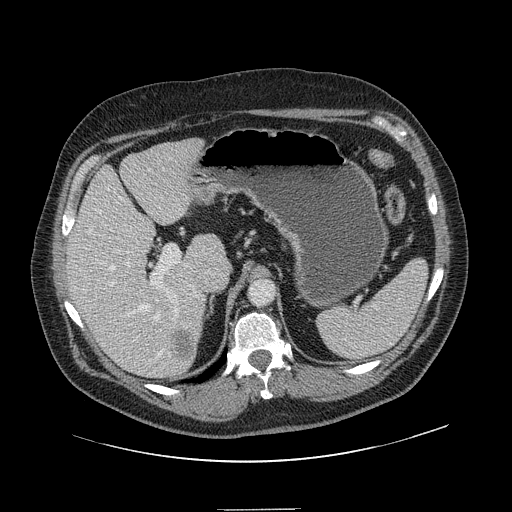
Contrast-enhanced abdominal CT, one axial slice. Slice 93 of 154 in the series (ordered by position). Intravenous contrast given. Soft-tissue window (W 400 / L 40 HU). 512 × 512 image matrix, field of view 451 × 451 mm. Male patient, age 61 years. From the clinical record (not read from this slice): diagnosis: colorectal cancer liver metastases, imaged before liver resection; multiple liver metastases: yes; largest metastasis: 2.6 cm; disease in both lobes: yes.
Outlined on this slice (outlined manually by an expert reader):
- hepatic veins: bounding box (x1, y1, x2, y2) in pixels: (88, 210, 179, 356)
- liver: (68, 140, 225, 378)
- planned liver remnant (the part of the liver to remain after resection): (68, 146, 225, 364)
- portal vein (with intrahepatic branches): (107, 186, 188, 301)
- liver metastasis: (174, 333, 196, 363)